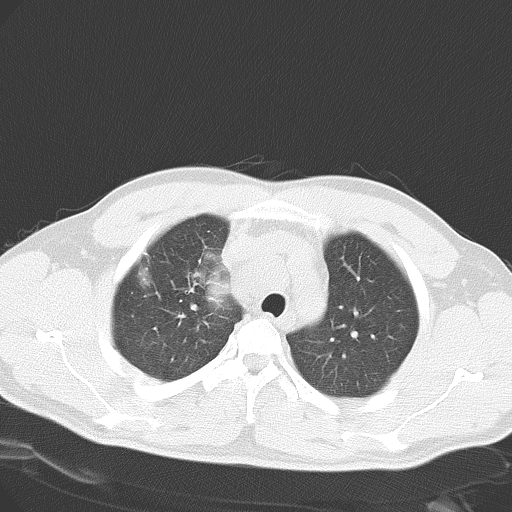
Chest CT, one axial slice; position 43 of 55 along the scan axis; reconstruction kernel B70f; lung window (W 1500 / L -600 HU); 5 mm slice thickness; 512 × 512 image matrix, field of view 346 × 346 mm. Male patient, age 32 years. From the clinical record (not read from this slice): clinical TNM (as recorded): T4 N3 M0; histopathological grade: G3.
Annotated regions visible in this slice (rectangle marked by the reading radiologist):
- lung tumour (recorded histology: small cell carcinoma): bounding box (x1, y1, x2, y2) in pixels: (192, 240, 240, 312)